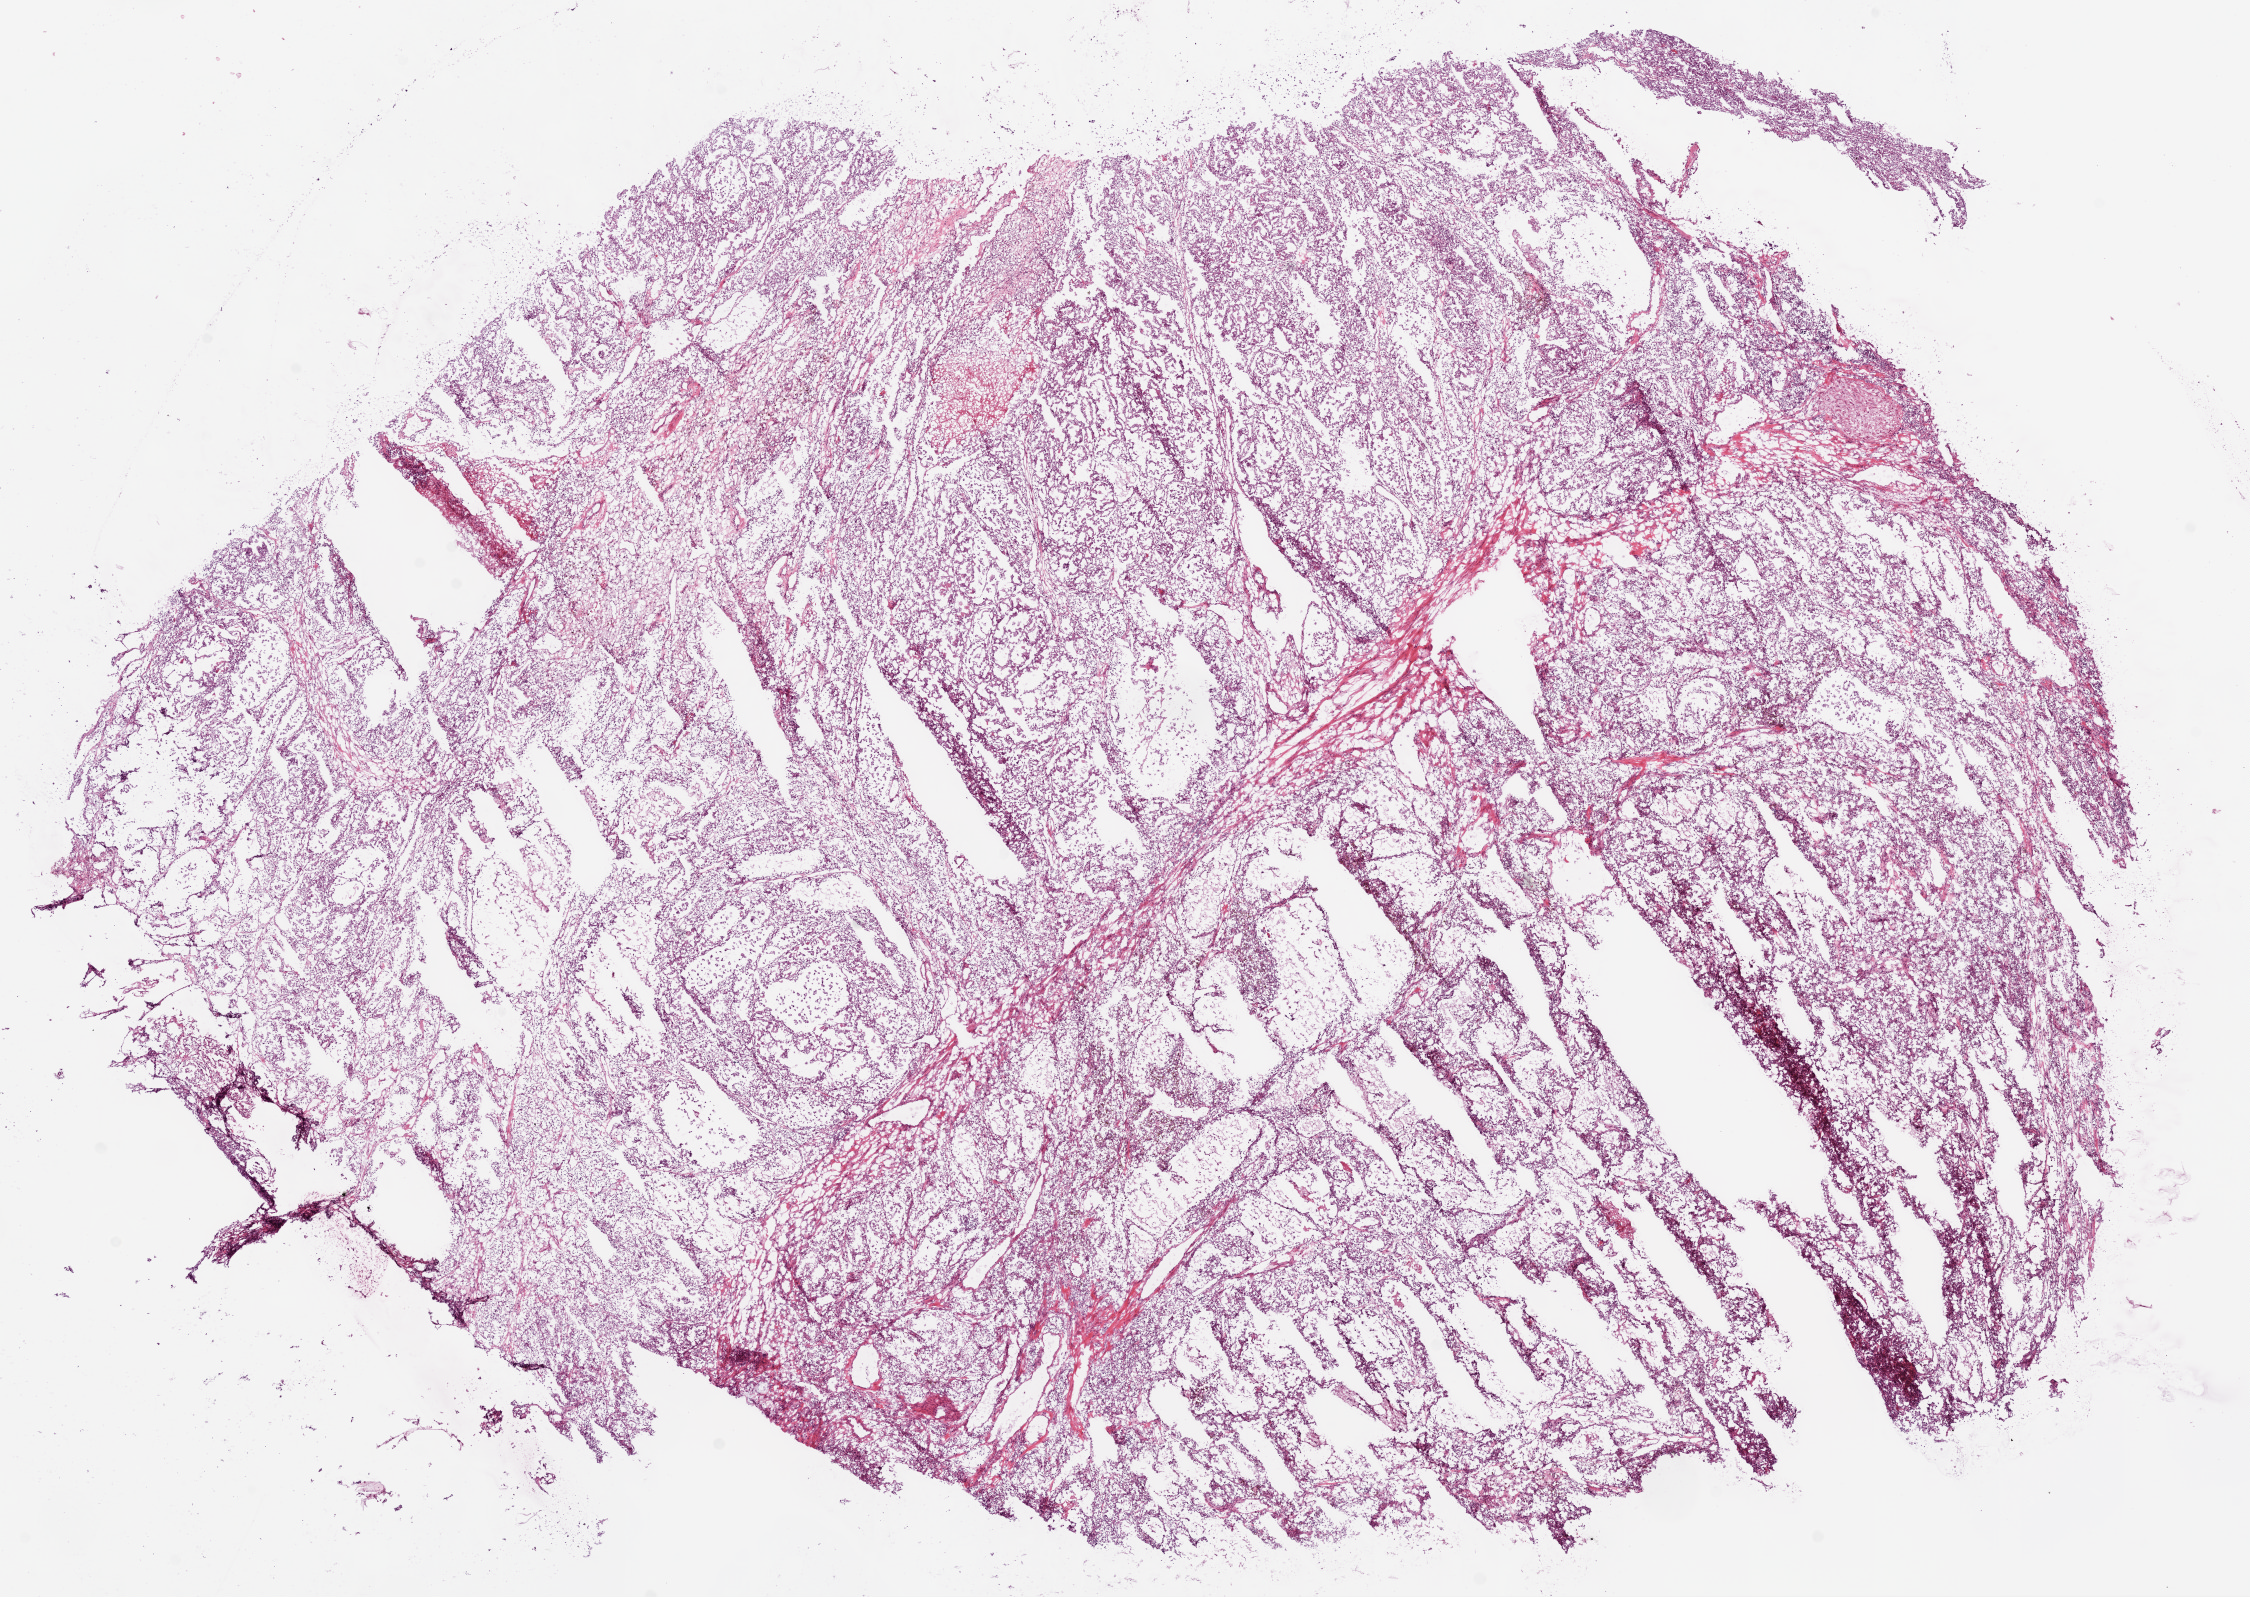
Hematoxylin and eosin (H&E) stained whole-slide image — low-resolution overview of the scanned area, about 18.1 x 12.8 mm, frozen section from the top of the tissue portion, sample: primary tumour, kidney. Patient: male, age at initial diagnosis 53 years. Histologic grade: G3 (poorly differentiated). Slide review estimates, as recorded: tumour cells 90%, tumour nuclei 75%, normal cells 0%, stromal cells 10%, necrosis 0%.
• laterality: right
• diagnosis: Clear cell adenocarcinoma, NOS
• AJCC pathologic stage: I (6th edition)